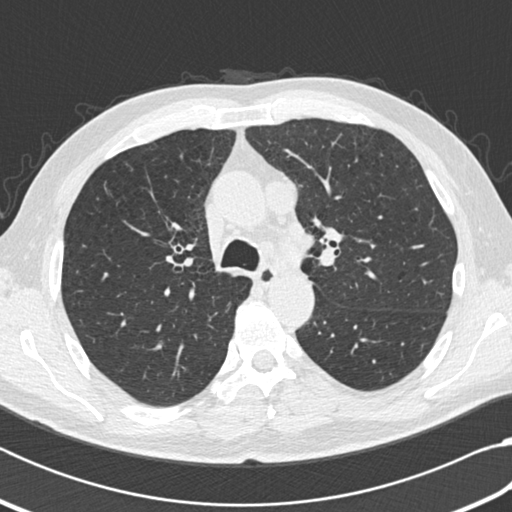
Low-dose screening chest CT, axial slice; third screening round (two years after baseline); lung window (W 1500 / L -600 HU); 2 mm slice thickness; standard (soft-tissue) reconstruction kernel (B30f); slice 66 of 207 in the series. Male, age 64 years at enrolment.
Expert reader's lesion annotation, bounding box <252,177,292,216> (left, top, right, bottom; pixels). Screening reader's record for this exam: no non-calcified nodule ≥4 mm recorded. Later outcome: lung cancer diagnosed 163 days after this screen — small cell carcinoma, NOS, mediastinum, stage IV (AJCC 6th edition).